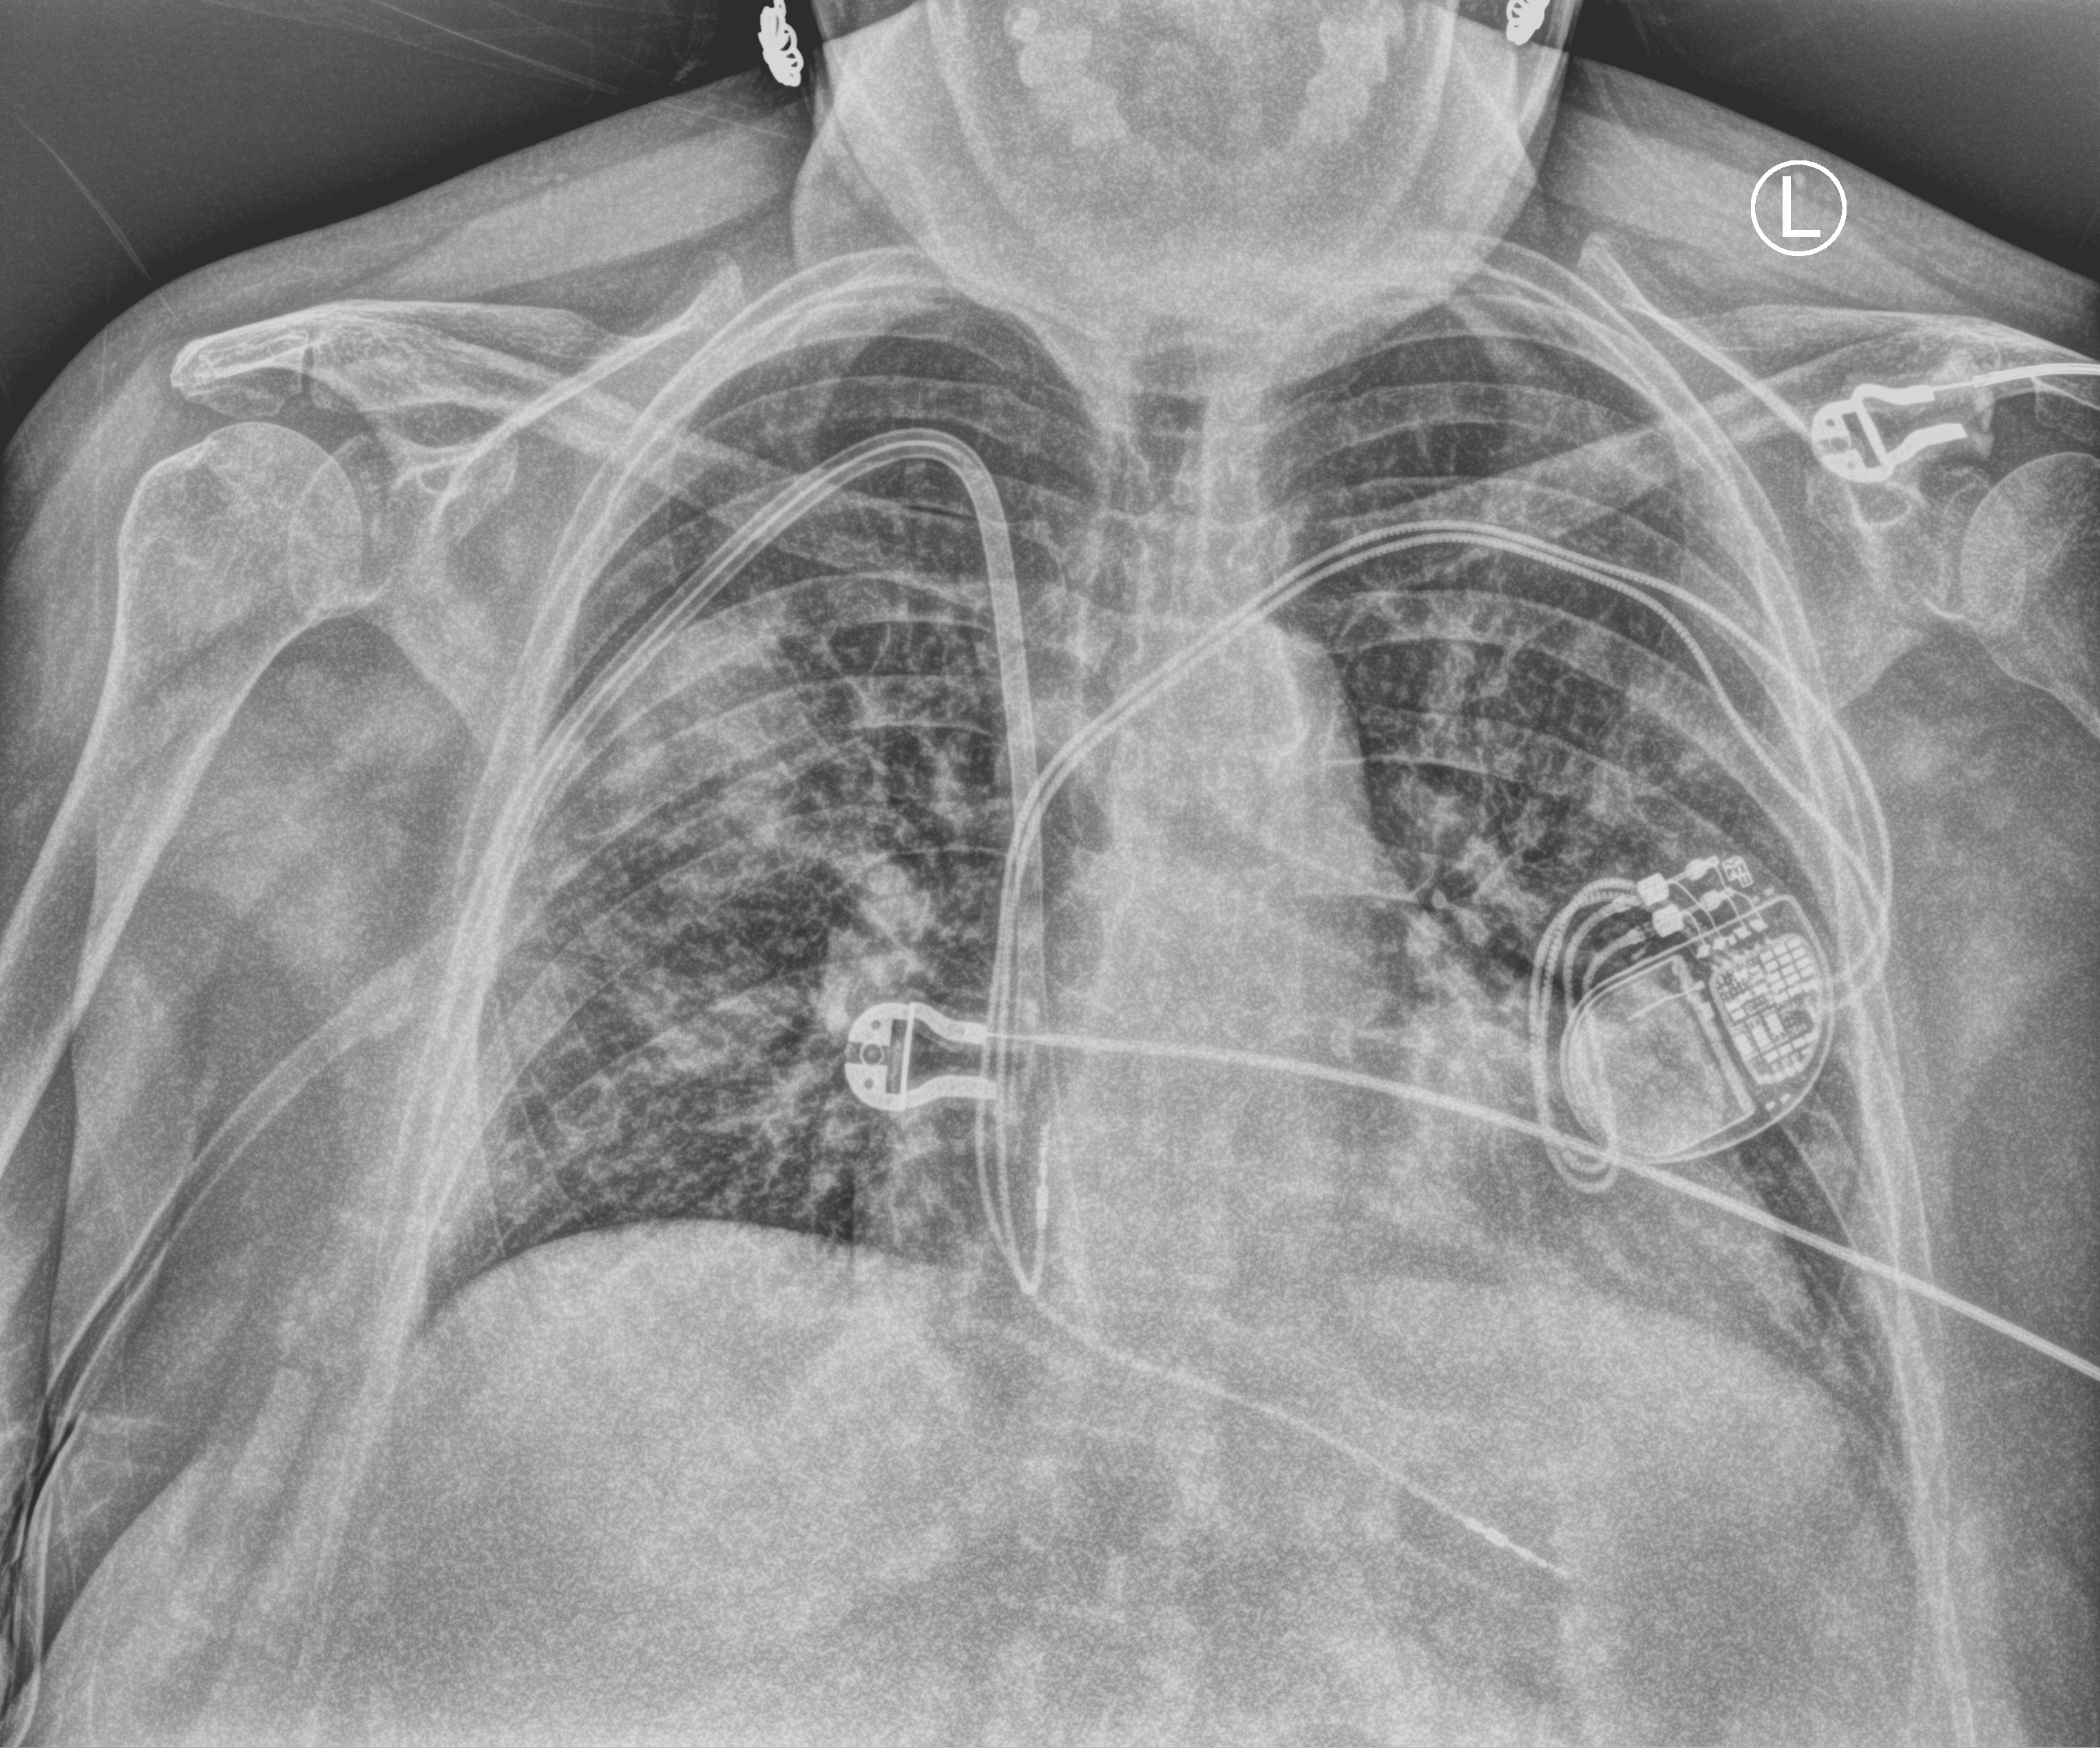
Portable chest radiograph, anteroposterior (AP) projection. Female patient hospitalised with COVID-19, age 60–74 years.
From the hospital-stay record, not from the radiograph (when in the stay this image was taken is not recorded):
- mechanically ventilated during this hospital stay: no
- admitted to intensive care during this hospital stay: no